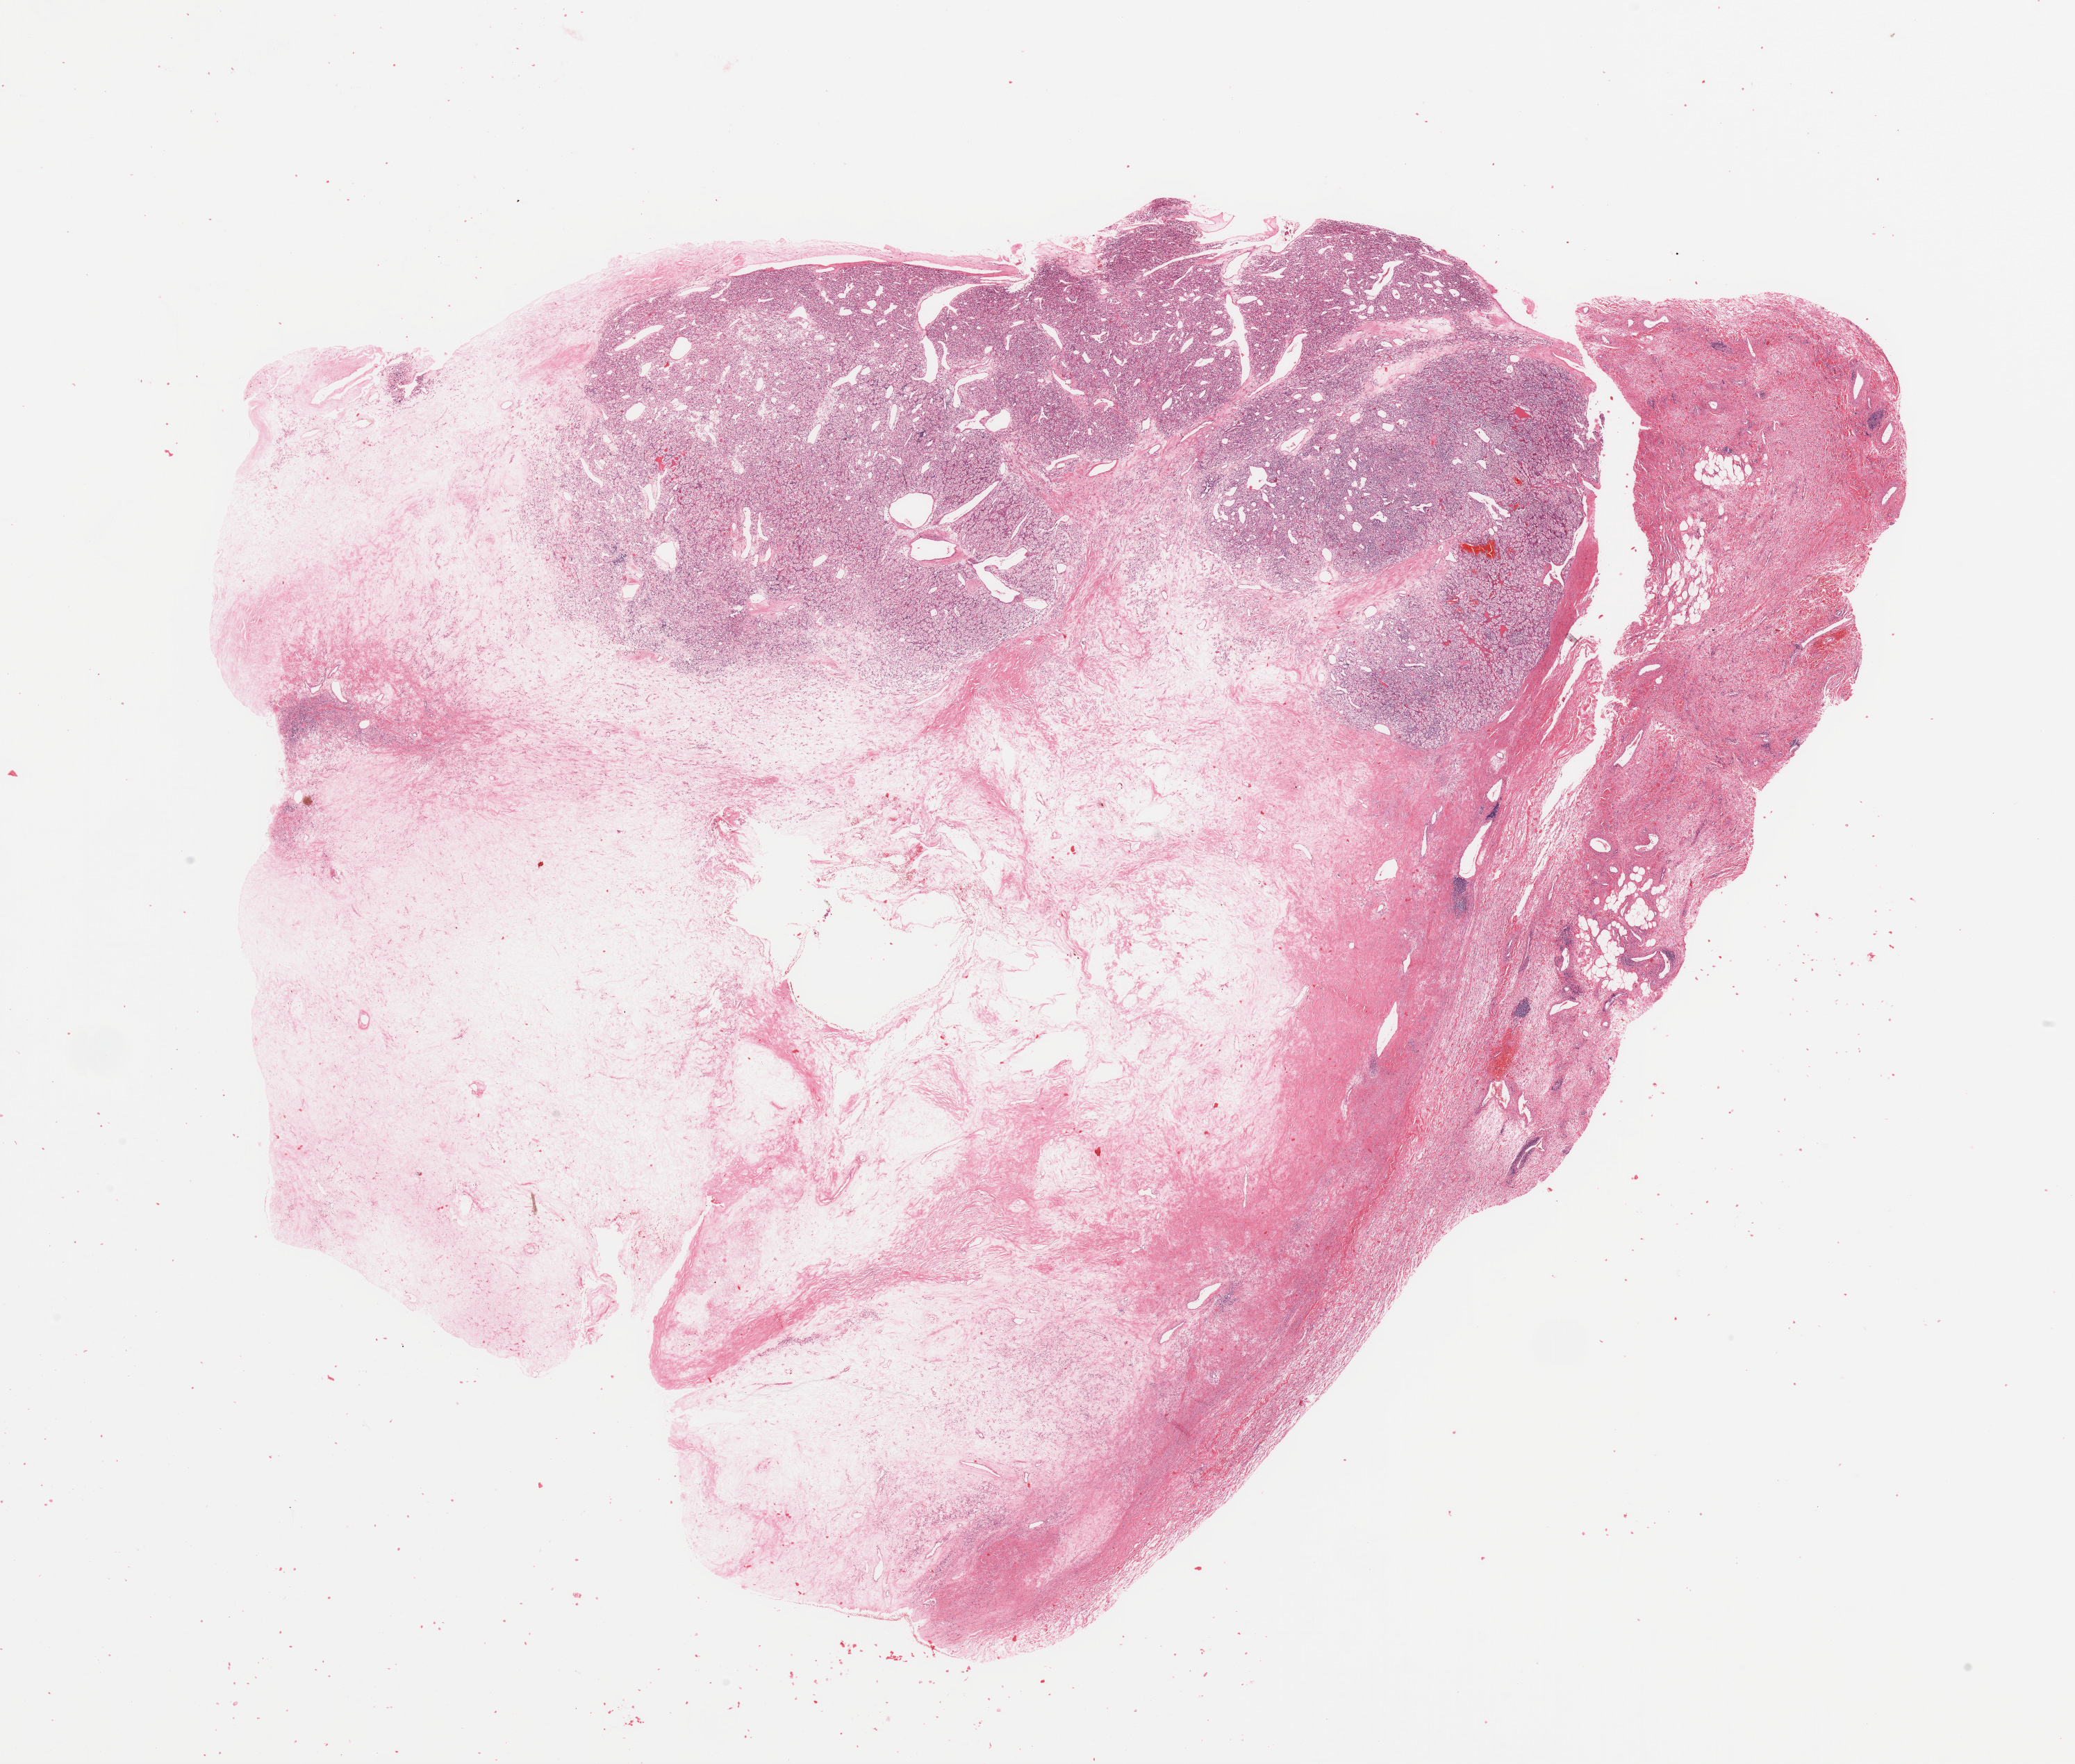
Hematoxylin and eosin (H&E) stained whole-slide image, a low-resolution overview of the entire scanned area, about 23.6 x 20.1 mm (slide scanned at 20x), tumour tissue sample, sampled site: kidney. Female, 57 y/o. Histologic grade: G2 (moderately differentiated). Slide review estimates, as recorded: tumour nuclei 80%, necrosis 30%.
- AJCC pathologic stage: I
- diagnosis: Renal cell carcinoma, NOS